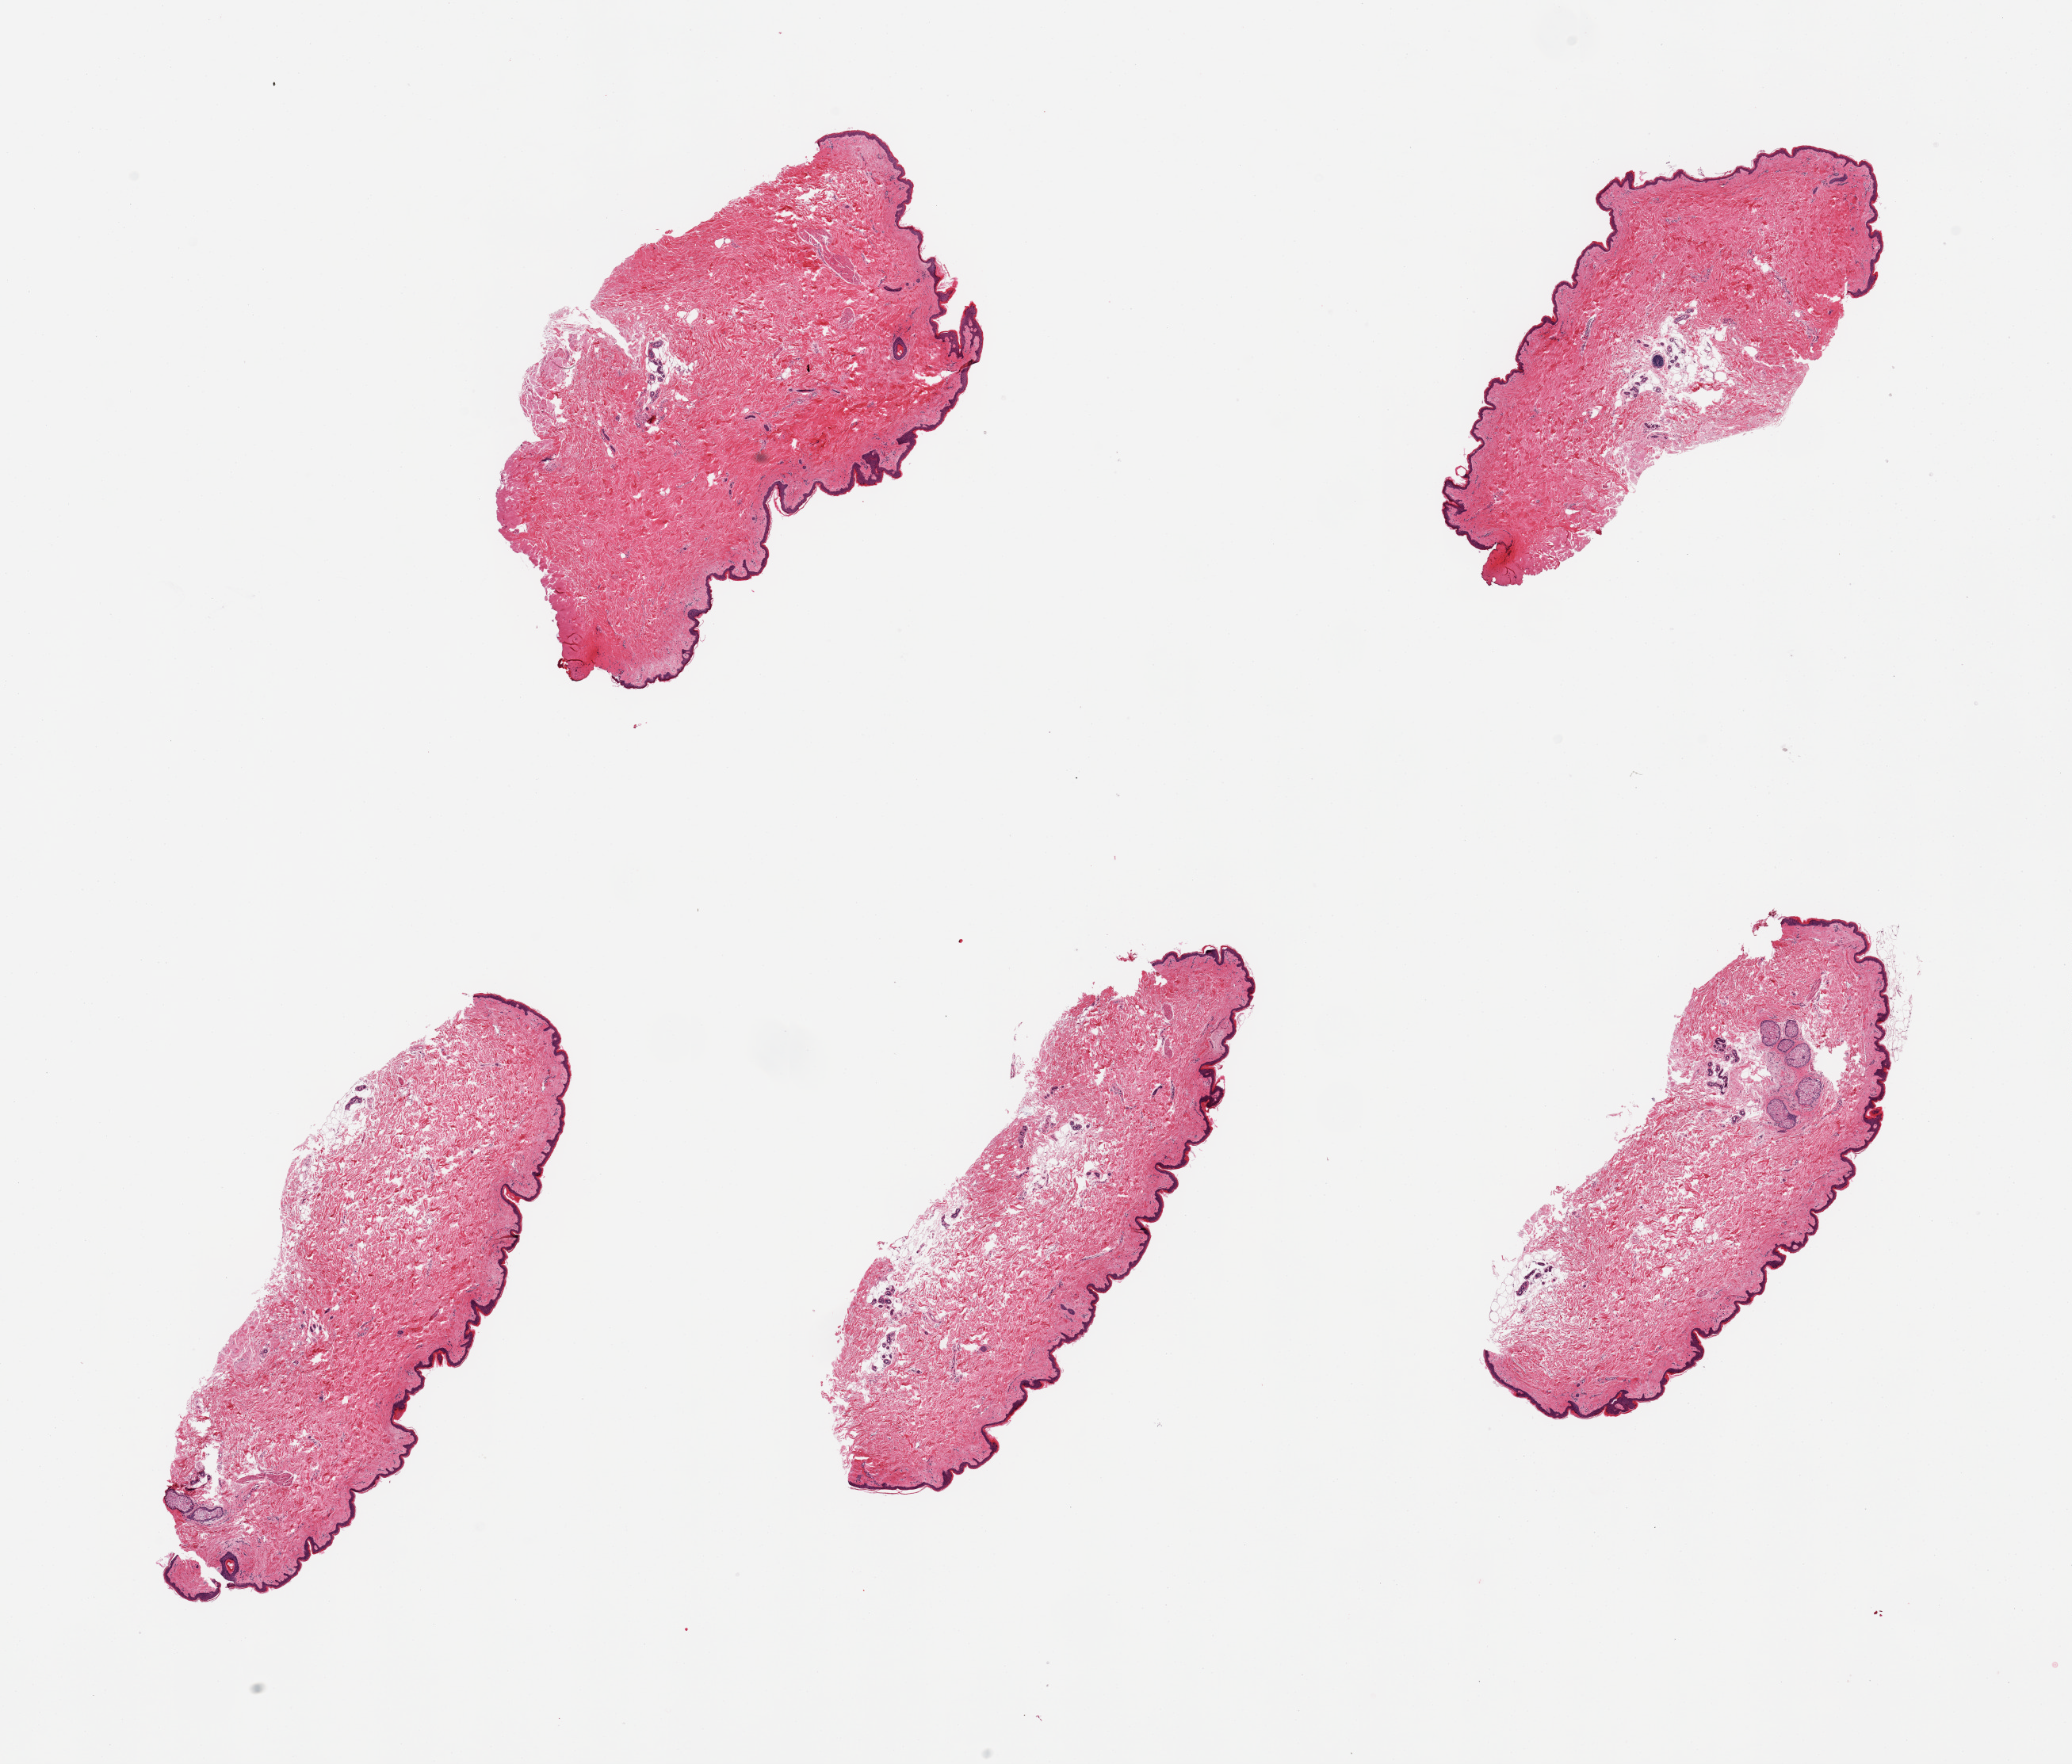
Whole-slide image, H&E stain, brightfield — whole scanned area (about 20.7 x 17.6 mm, from a 20x scan) shown as a low-resolution overview; PAXgene-fixed paraffin-embedded (PFPE) section; section of skin of suprapubic region (target tissue); tissue donor sample. Female donor.
Review note (as recorded): 5 pieces, minimal dermal fat, squamous epithelium is ~30-35 microns.